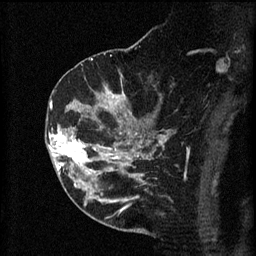
Breast MRI (dynamic contrast-enhanced), one sagittal slice; position 35 of 60 along the scan axis; 3 images stored at this slice position (order not interpretable as contrast timing); 1.5 T; TE 4.2 ms, TR 8.2 ms; 256 × 256 image matrix. Female patient, age 49 years.
Outlined on this slice (semi-automatically segmented with operator editing):
- analysis volume of interest (the breast-tissue region the enhancement analysis was run in; not a lesion): bounding box [x1, y1, x2, y2] px = [45, 126, 105, 177]
- tumour enhancement mask (voxels above the 70 % enhancement threshold inside the analysis volume of interest): [49, 126, 101, 175]